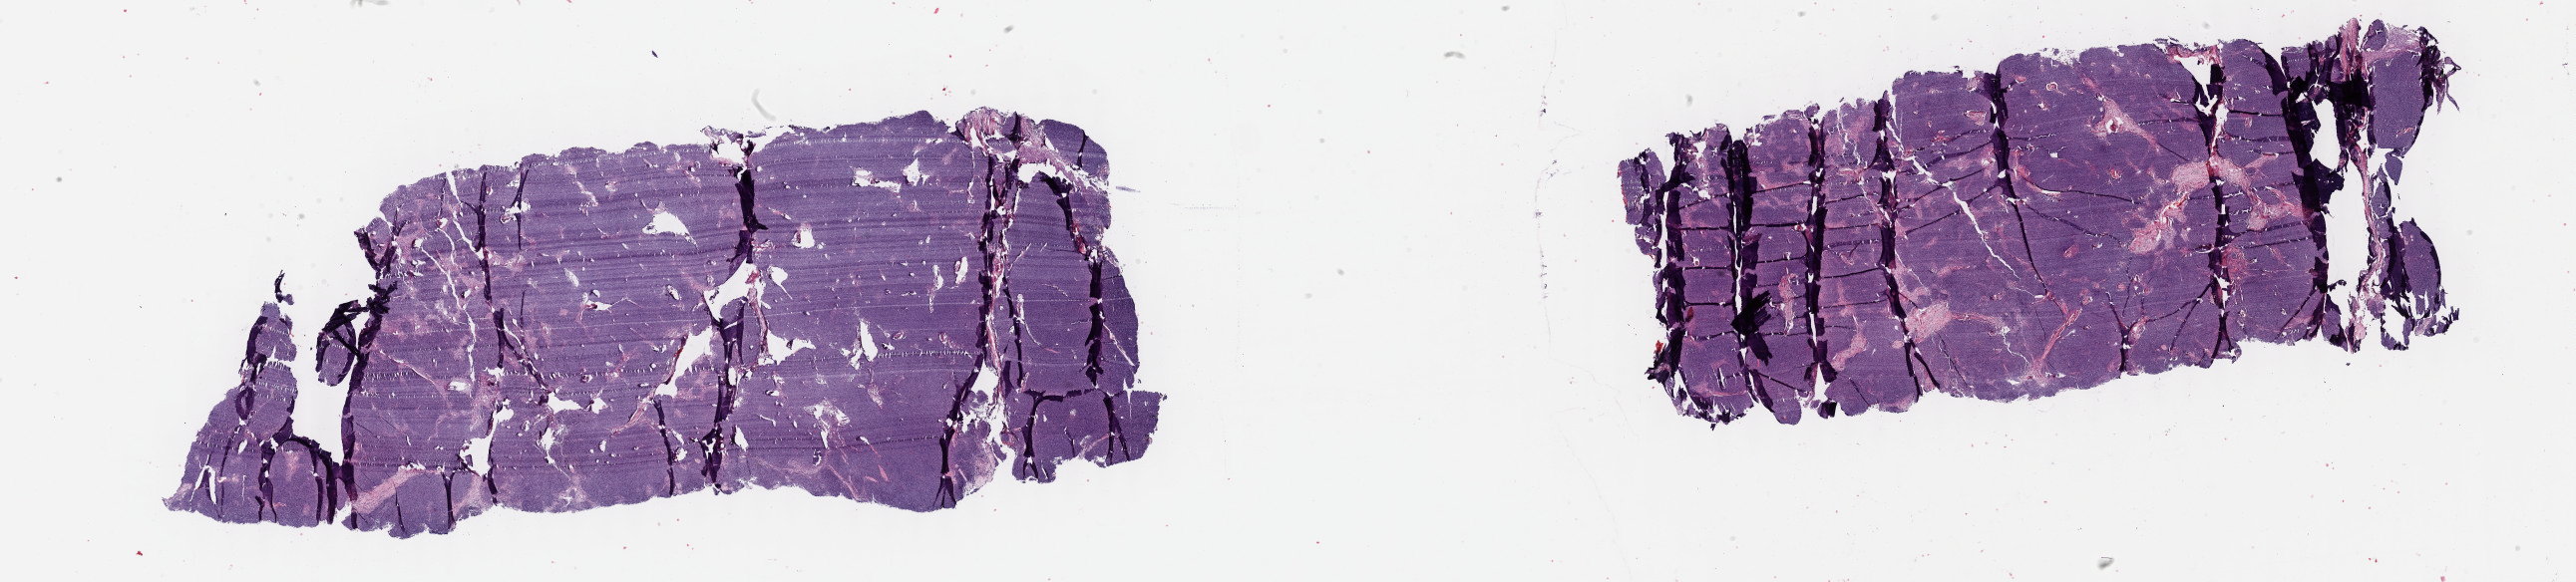
Digitized H&E-stained tissue section (whole slide) — a low-resolution overview of the entire scanned area, about 41.8 x 9.4 mm (slide scanned at 40x); formalin-fixed paraffin-embedded (FFPE) diagnostic section; sample: primary tumour, thymus. Female patient; age at initial diagnosis 57 years.
Diagnosis: Thymoma, type AB, malignant.